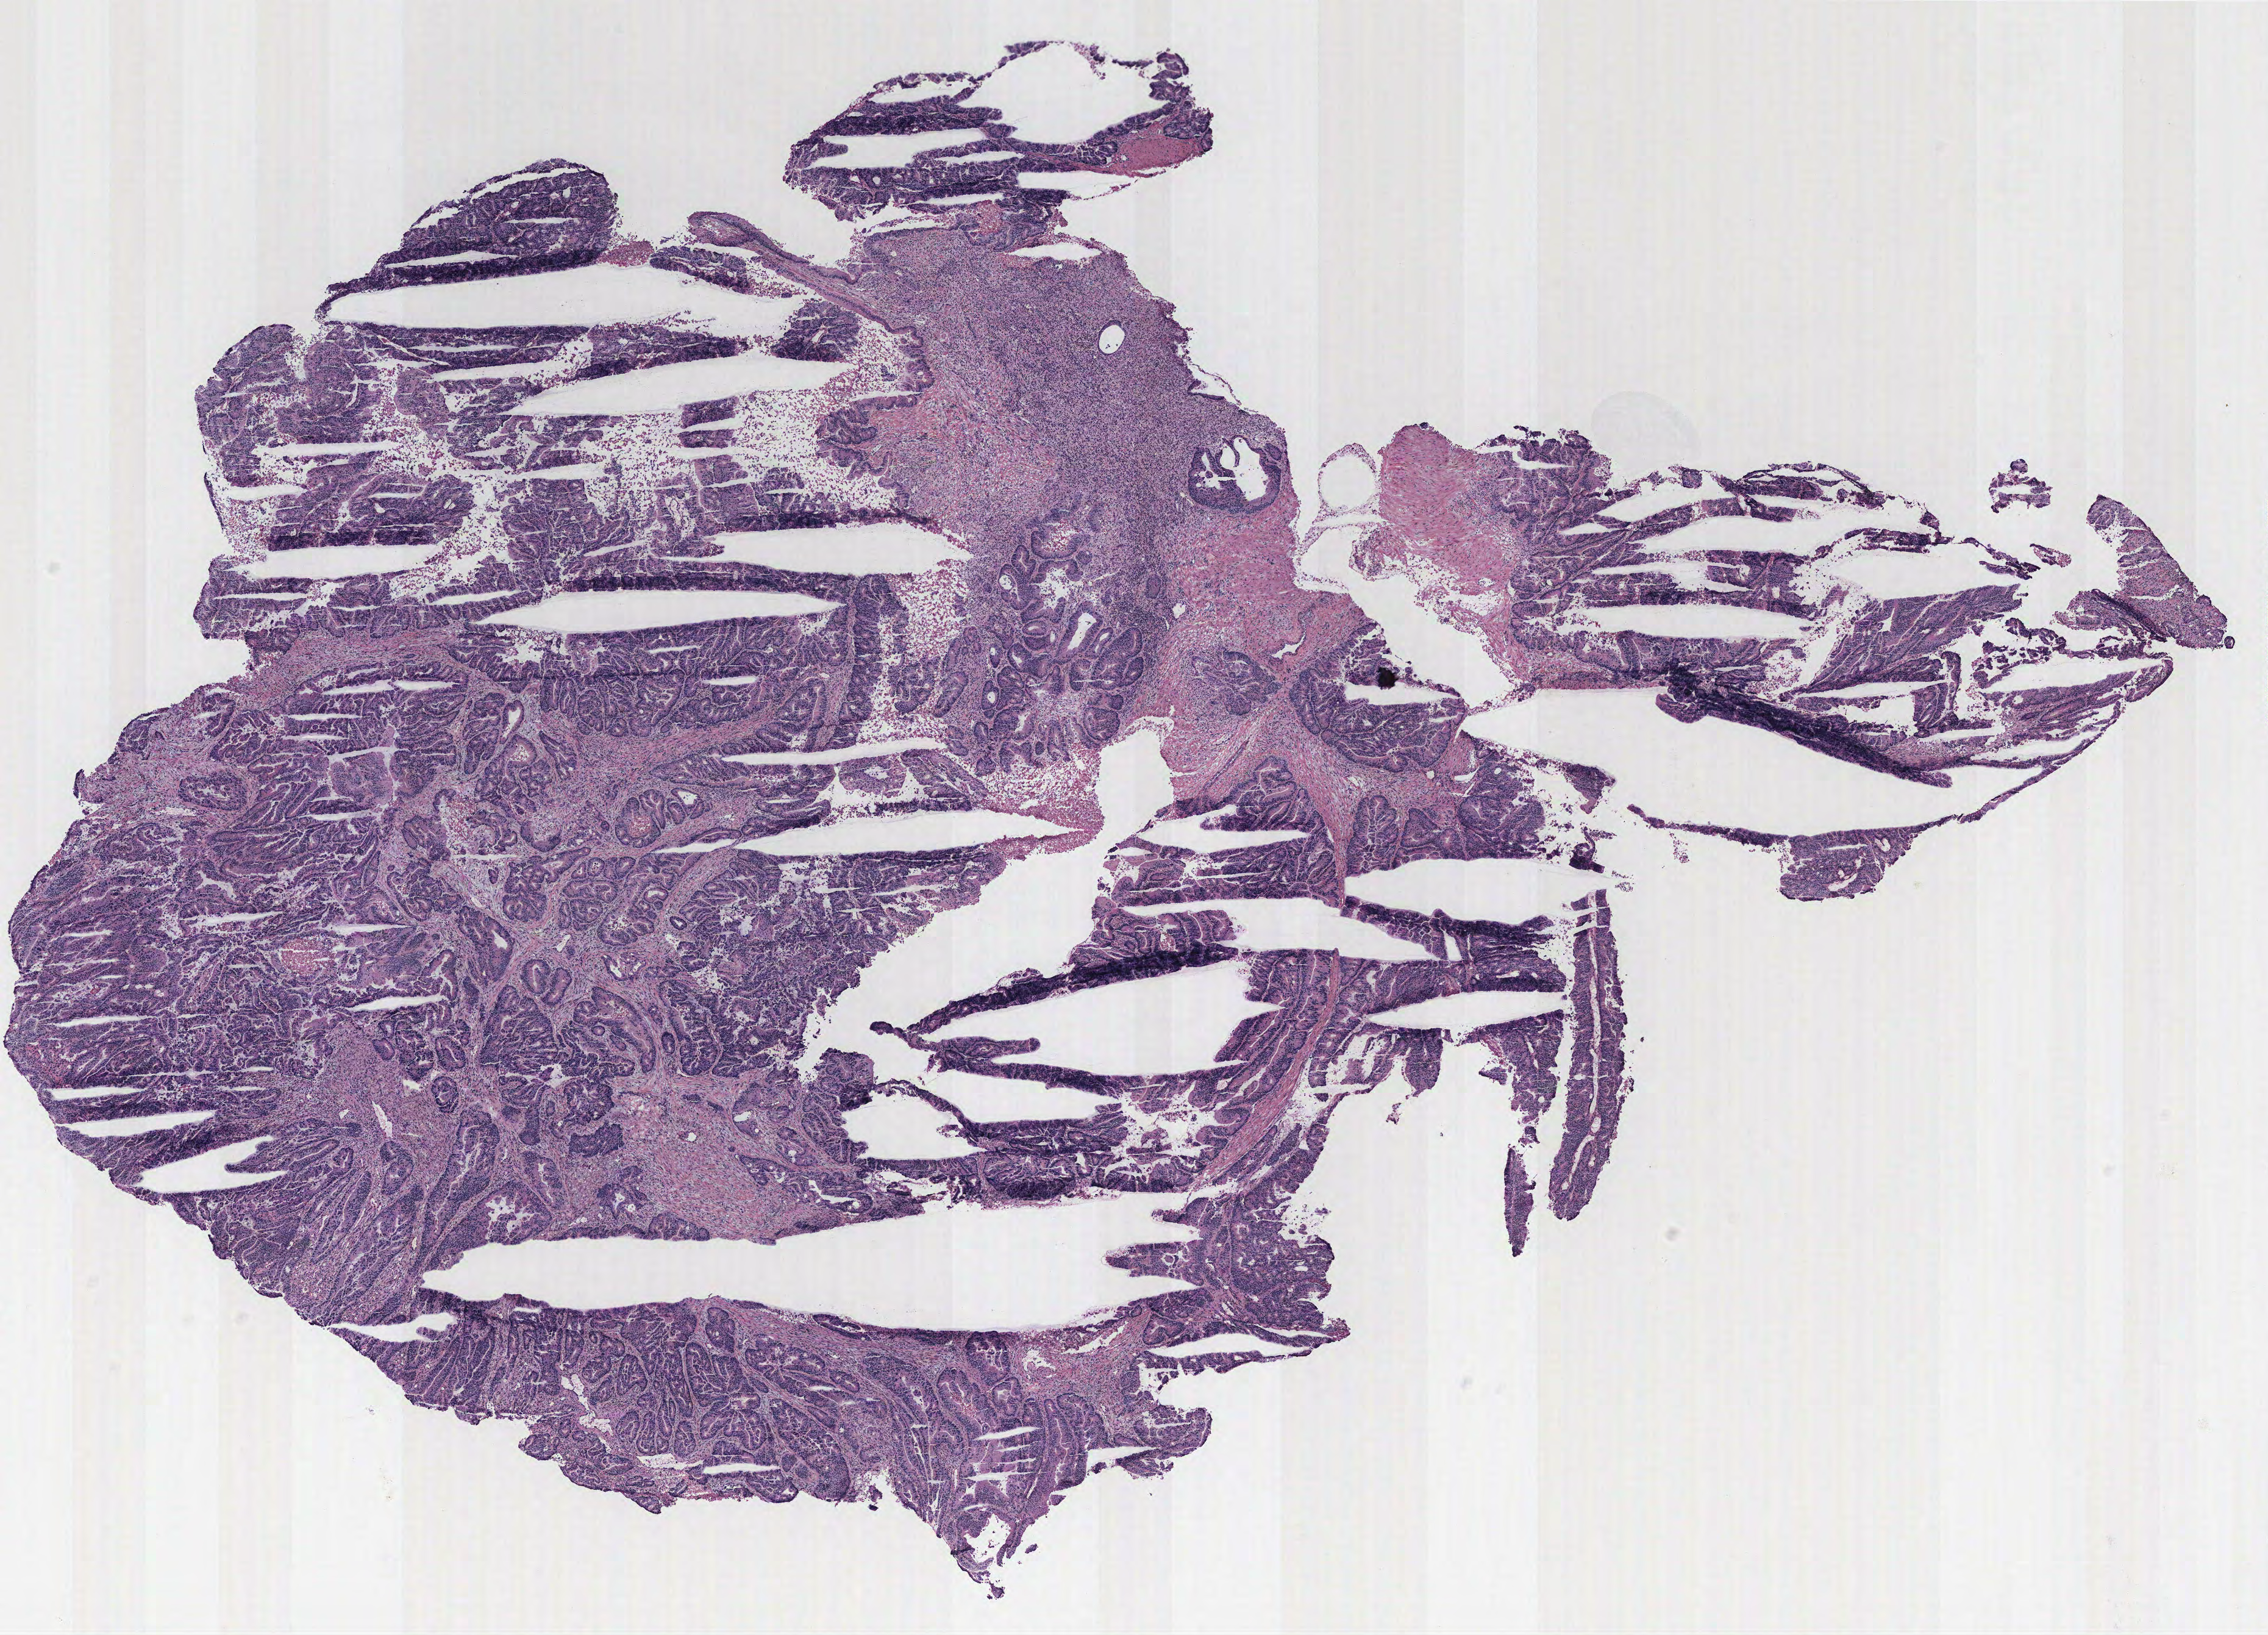
Digitized H&E-stained tissue section (whole slide) — a low-resolution overview of the entire scanned area, about 14.9 x 10.7 mm; colon, tumour tissue. 56-year-old male patient.
AJCC pathologic stage: I. Diagnosis: Adenocarcinoma, NOS. Primary tumour site (as recorded): colon.